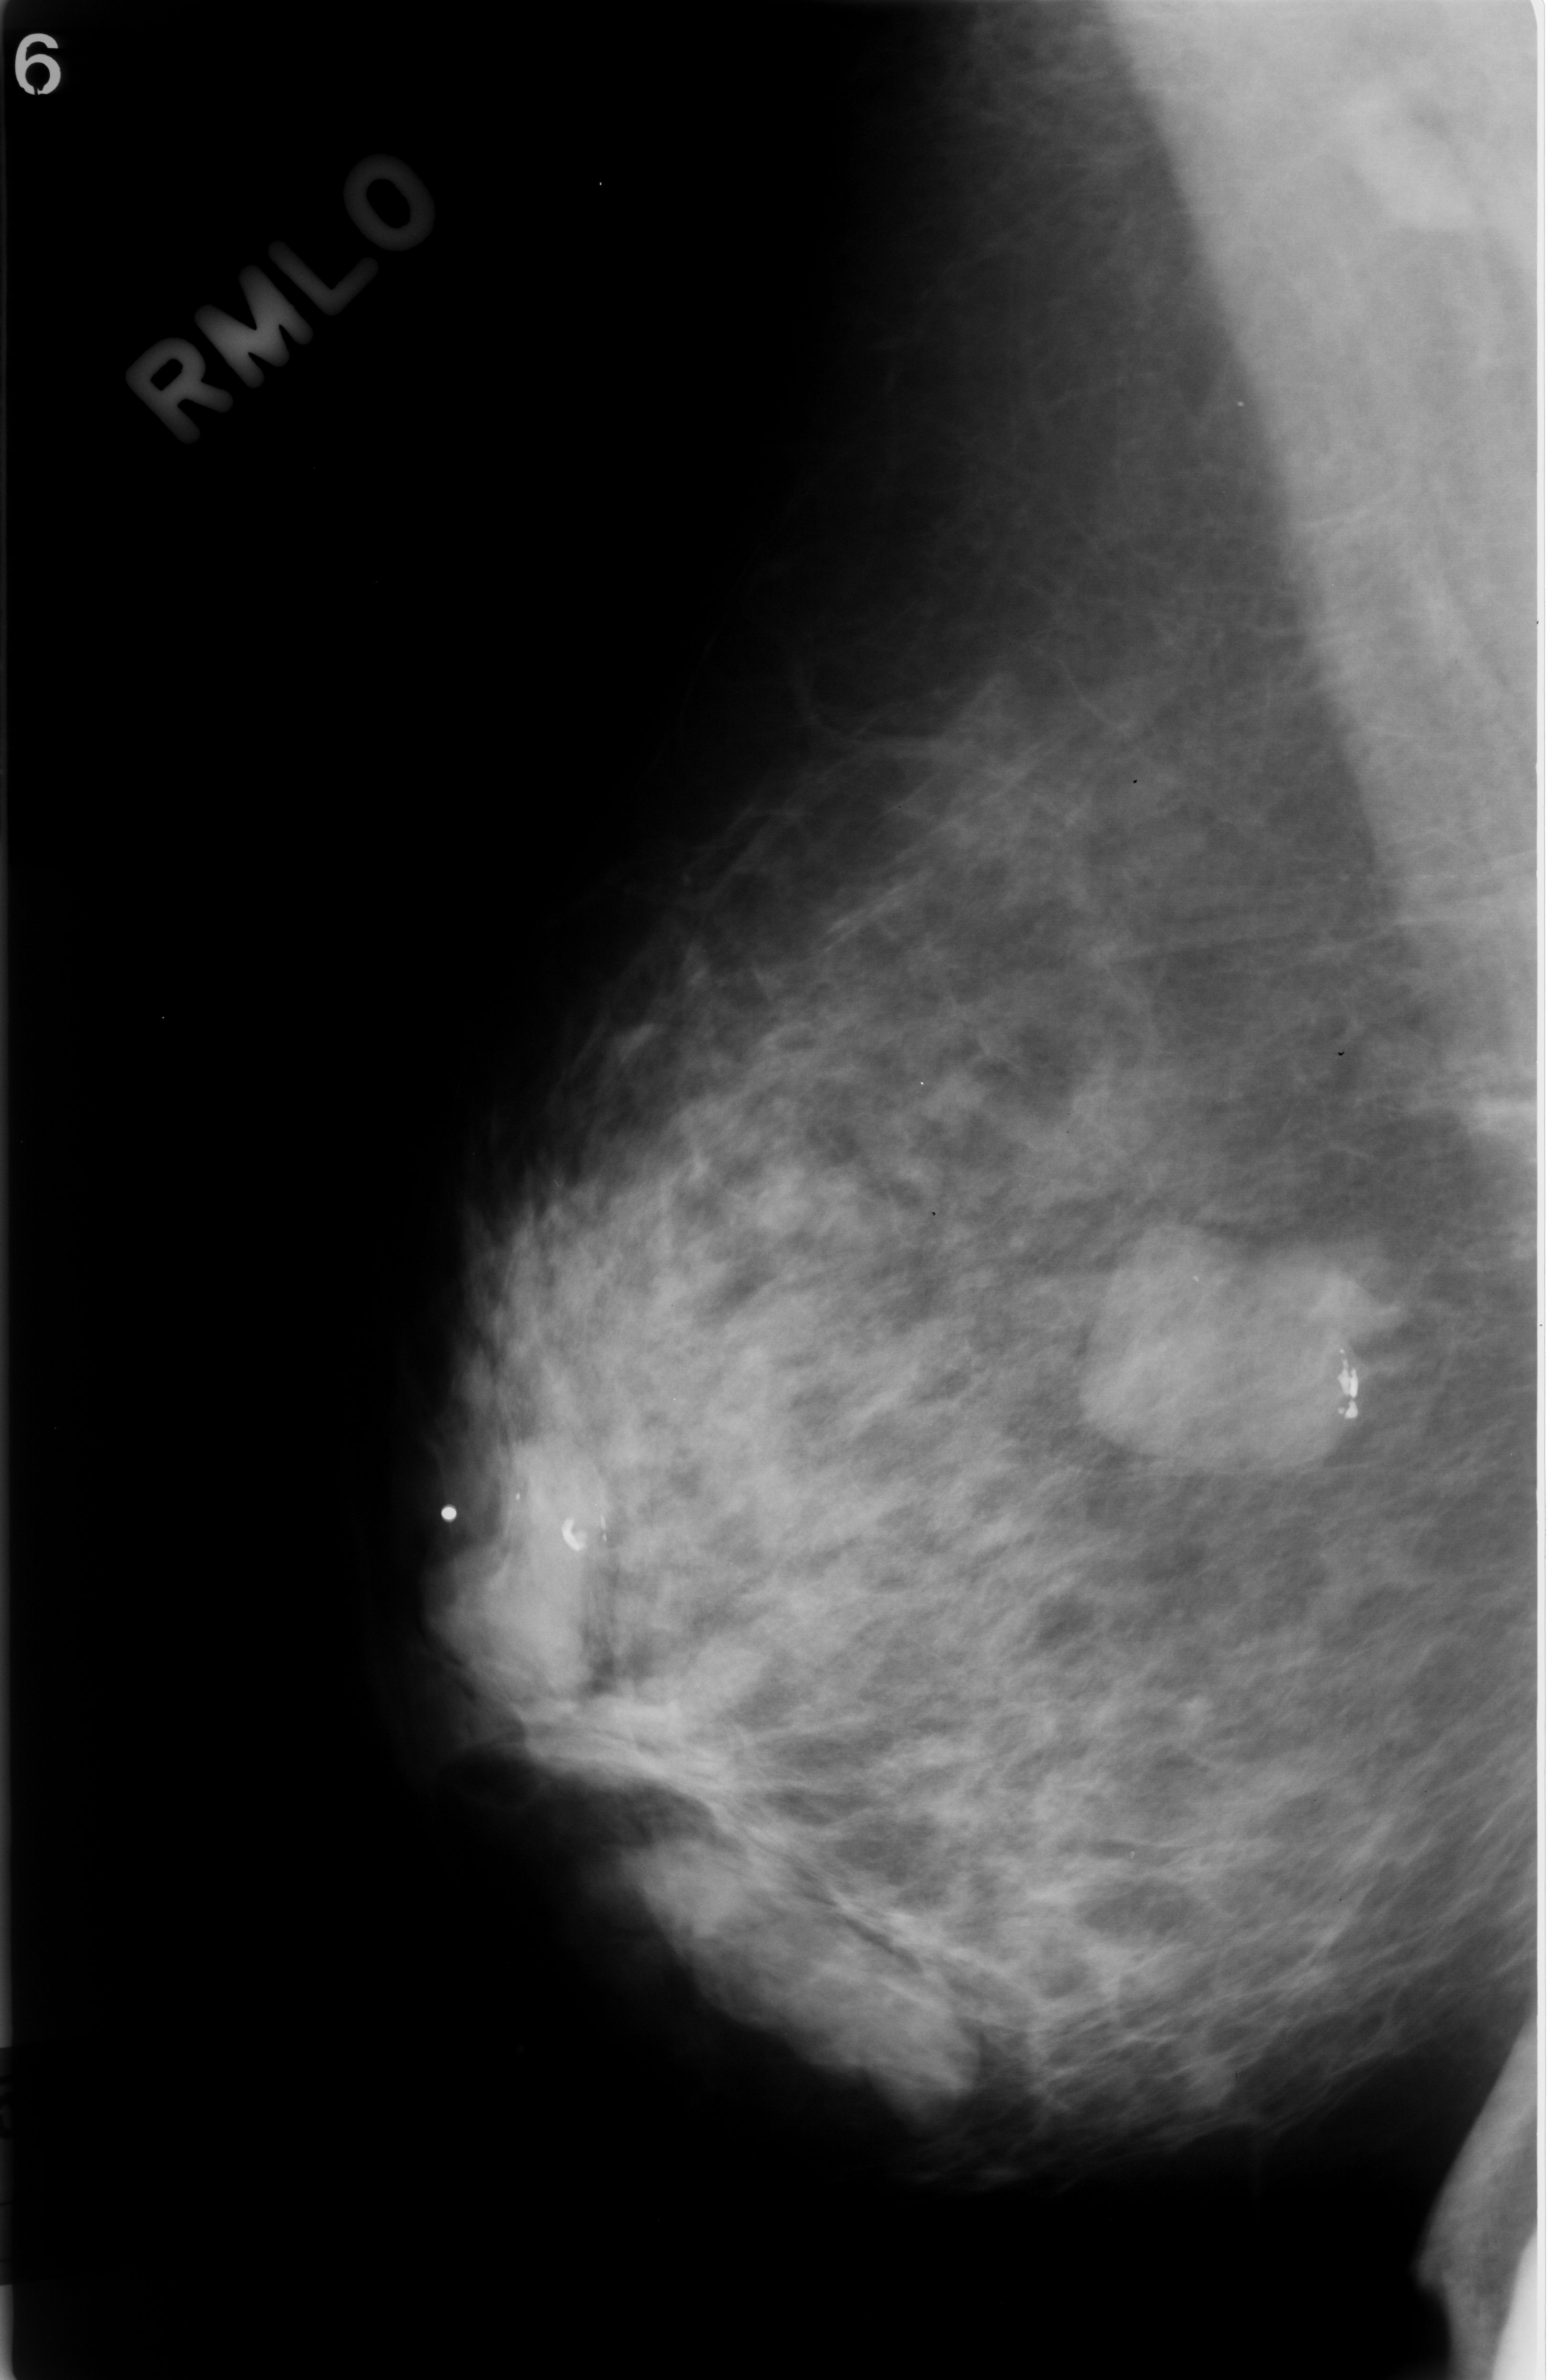
Scanned film-screen mammogram. Right breast. Mediolateral oblique (MLO) view. Breast composition: scattered fibroglandular densities (BI-RADS density category 2 of 4). 1548 × 2380 image matrix.
Expert-marked regions of interest on this film, with their recorded descriptors:
- Finding 1 of 2: mass, shape oval, margins circumscribed; BI-RADS assessment category 3; subtlety rating 5 on a 1 (subtle) to 5 (obvious) scale; pathology result (as recorded, not read from the image): benign: bounding box (x1, y1, x2, y2) in pixels: (417, 1439, 631, 1760)
- Finding 2 of 2: mass, shape lobulated, margins circumscribed; BI-RADS assessment category 3; pathology result (as recorded, not read from the image): benign: (1078, 1216, 1359, 1468)